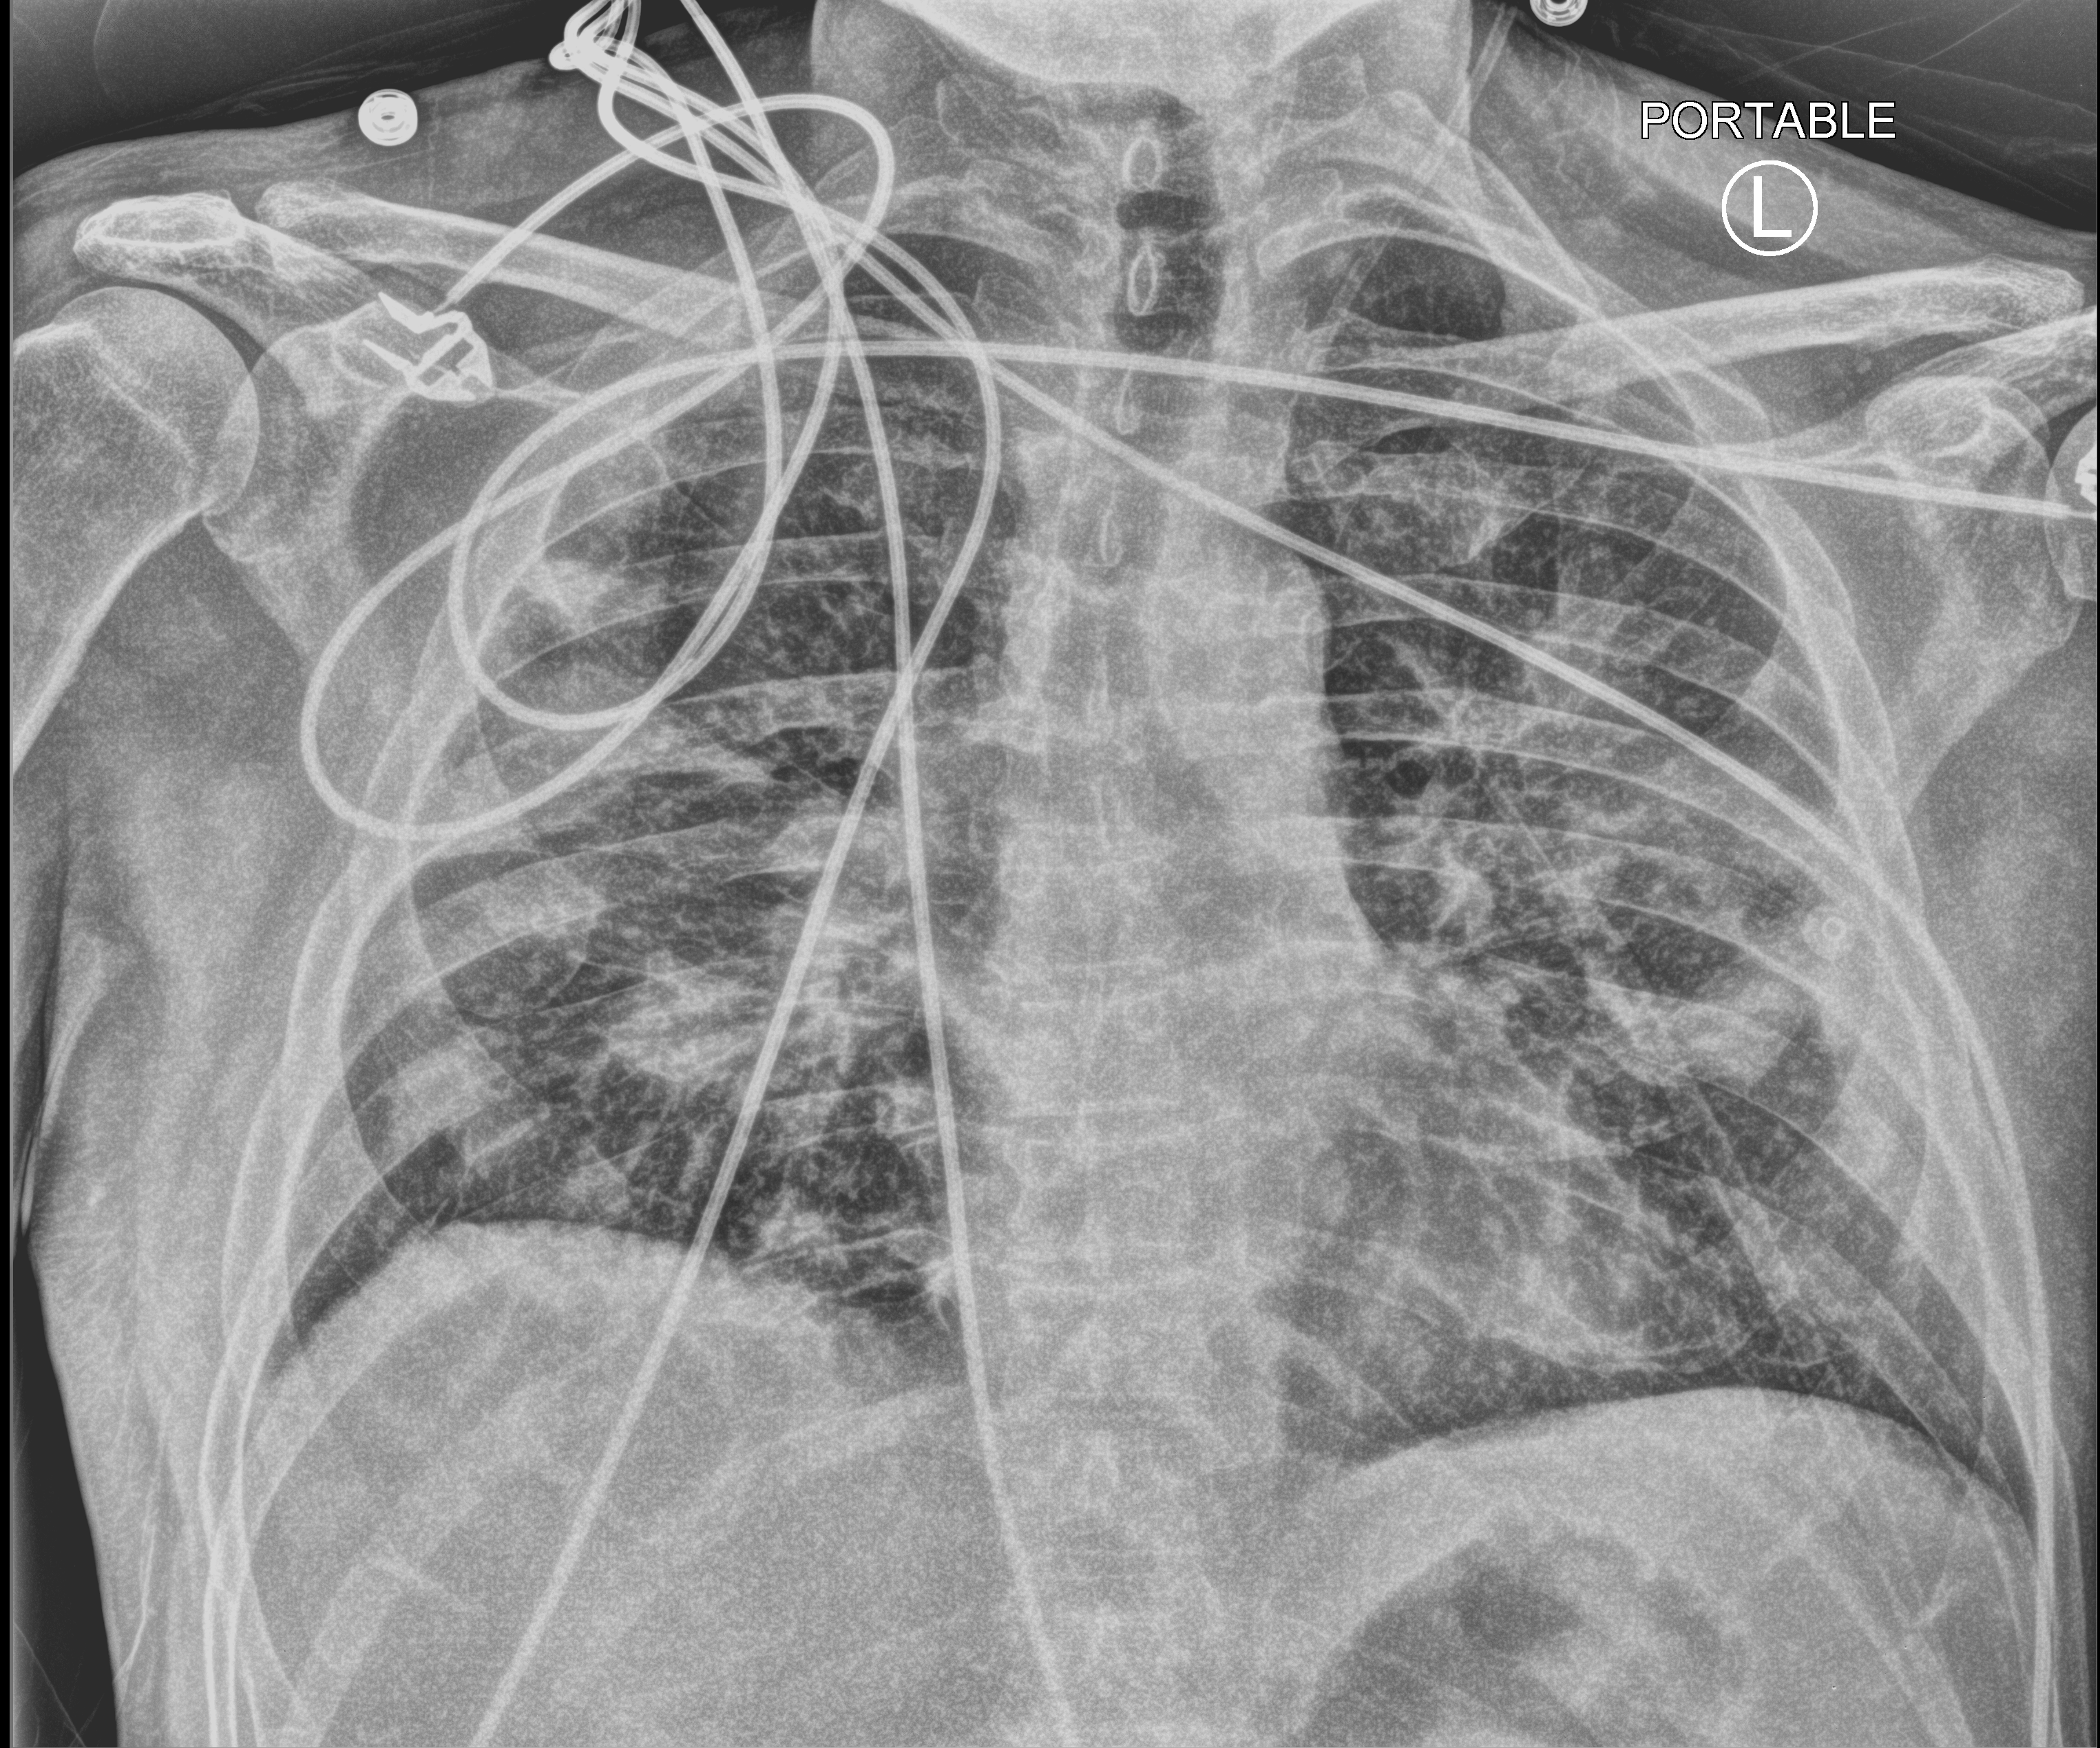
Chest X-ray (portable). Patient hospitalised with COVID-19; male, aged 18–59 years.
Hospital-stay facts (about this admission, not read from this image; timing relative to this image not recorded):
- mechanically ventilated during this hospital stay: no